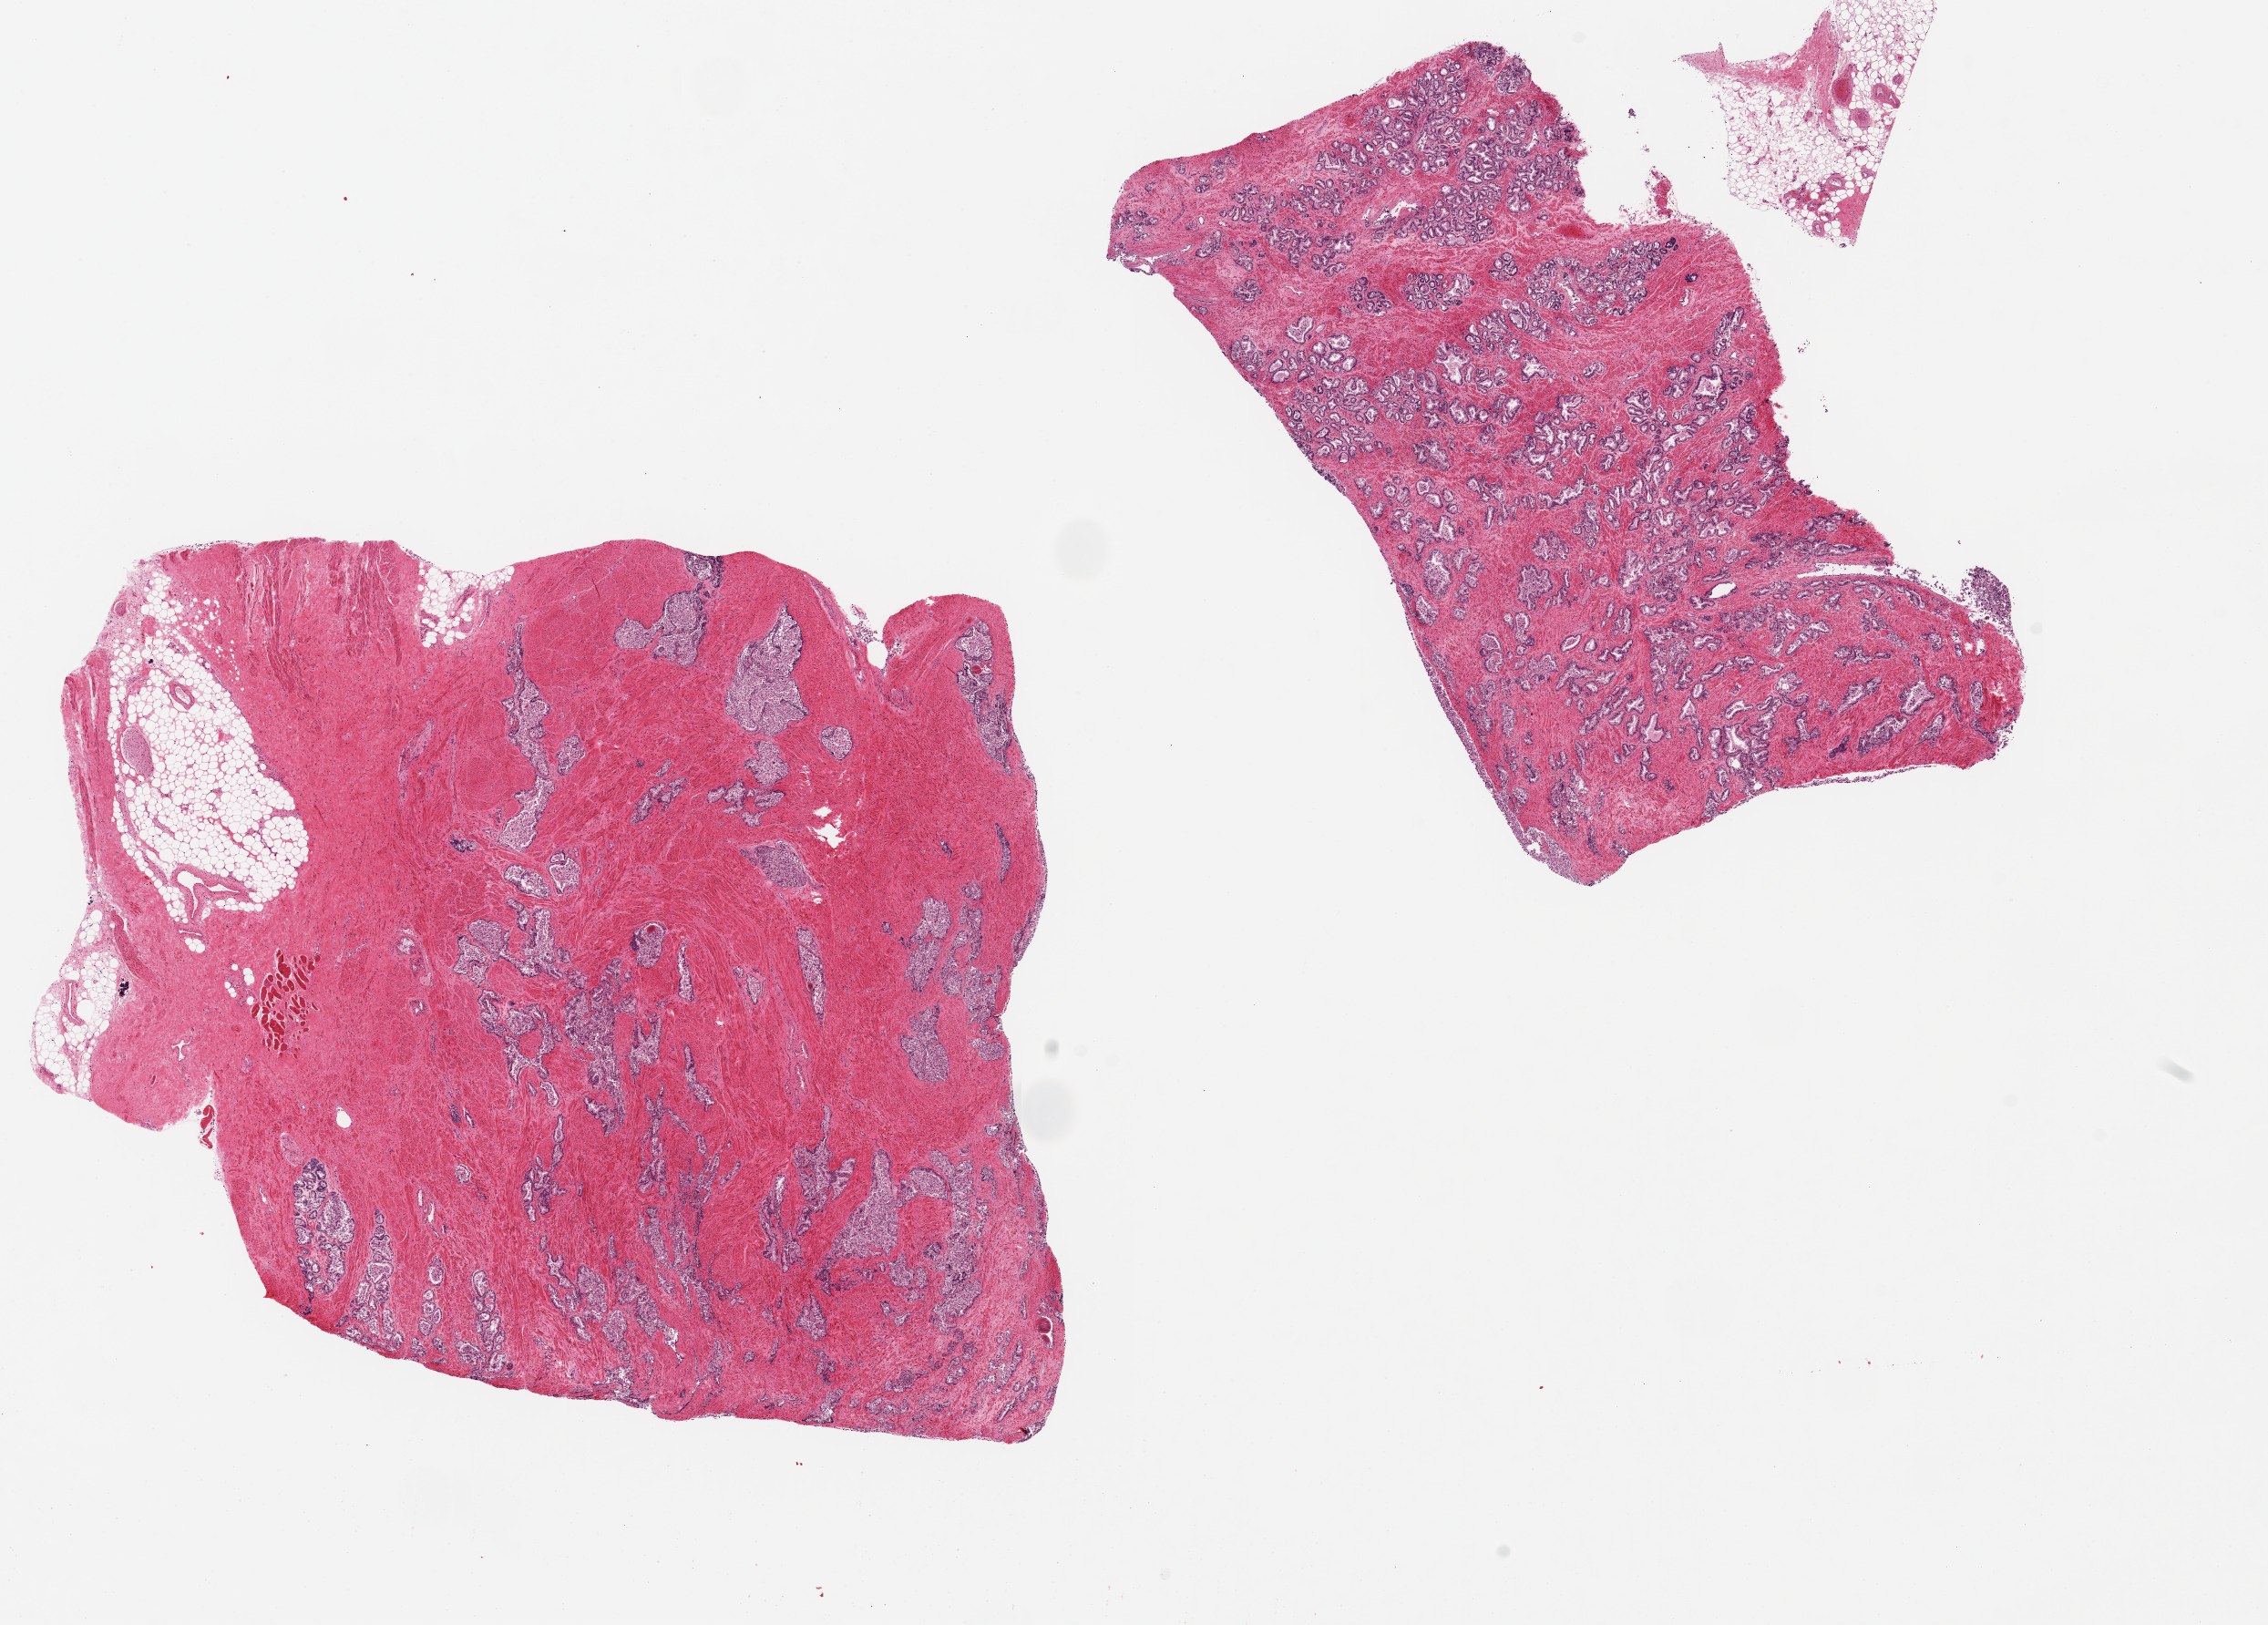
Digitized H&E-stained section — low-resolution overview of the scanned area, about 19.7 x 14.1 mm (acquisition: 20x scan); PAXgene-fixed, paraffin-embedded tissue; target tissue: prostate; tissue donor sample.
• pathologist's review note for this sample: 2 pieces, 9x7.5 & 7x7mm; prominent glandular hyperplasia; on aliquot well -preserved (enclrcled/), the other more autolyzed (score 2-3)